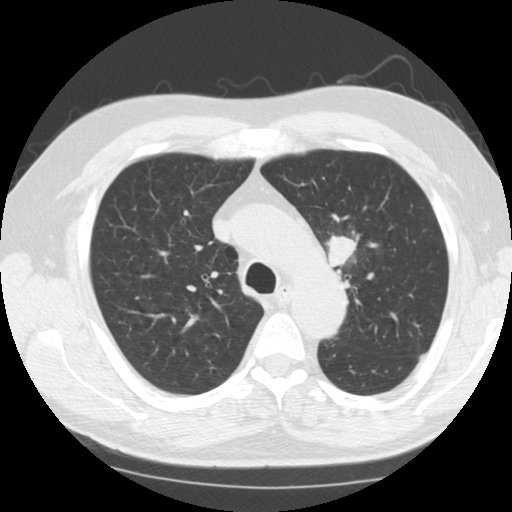
Low-dose screening chest CT, axial slice, third screening round (two years after baseline), lung window (W 1500 / L -600 HU), 2.5 mm slice thickness, standard (soft-tissue) reconstruction kernel (STANDARD), 120 kVp. Male participant, aged 60 years at enrolment.
- Expert-annotated lung lesion, bounding box <317,226,370,284> (left, top, right, bottom; pixels).
- Reader record for this screening exam (exam-level; its link to the box is not recorded): non-calcified nodule or mass ≥4 mm, left upper lobe, 24 × 21 mm, smooth margins, soft tissue attenuation, pre-existing on the prior screen: no.
- Later outcome: lung cancer diagnosed 14 days after this screen — small cell carcinoma, NOS, left upper lobe, stage IIA (AJCC 6th edition), 26 mm at pathology.